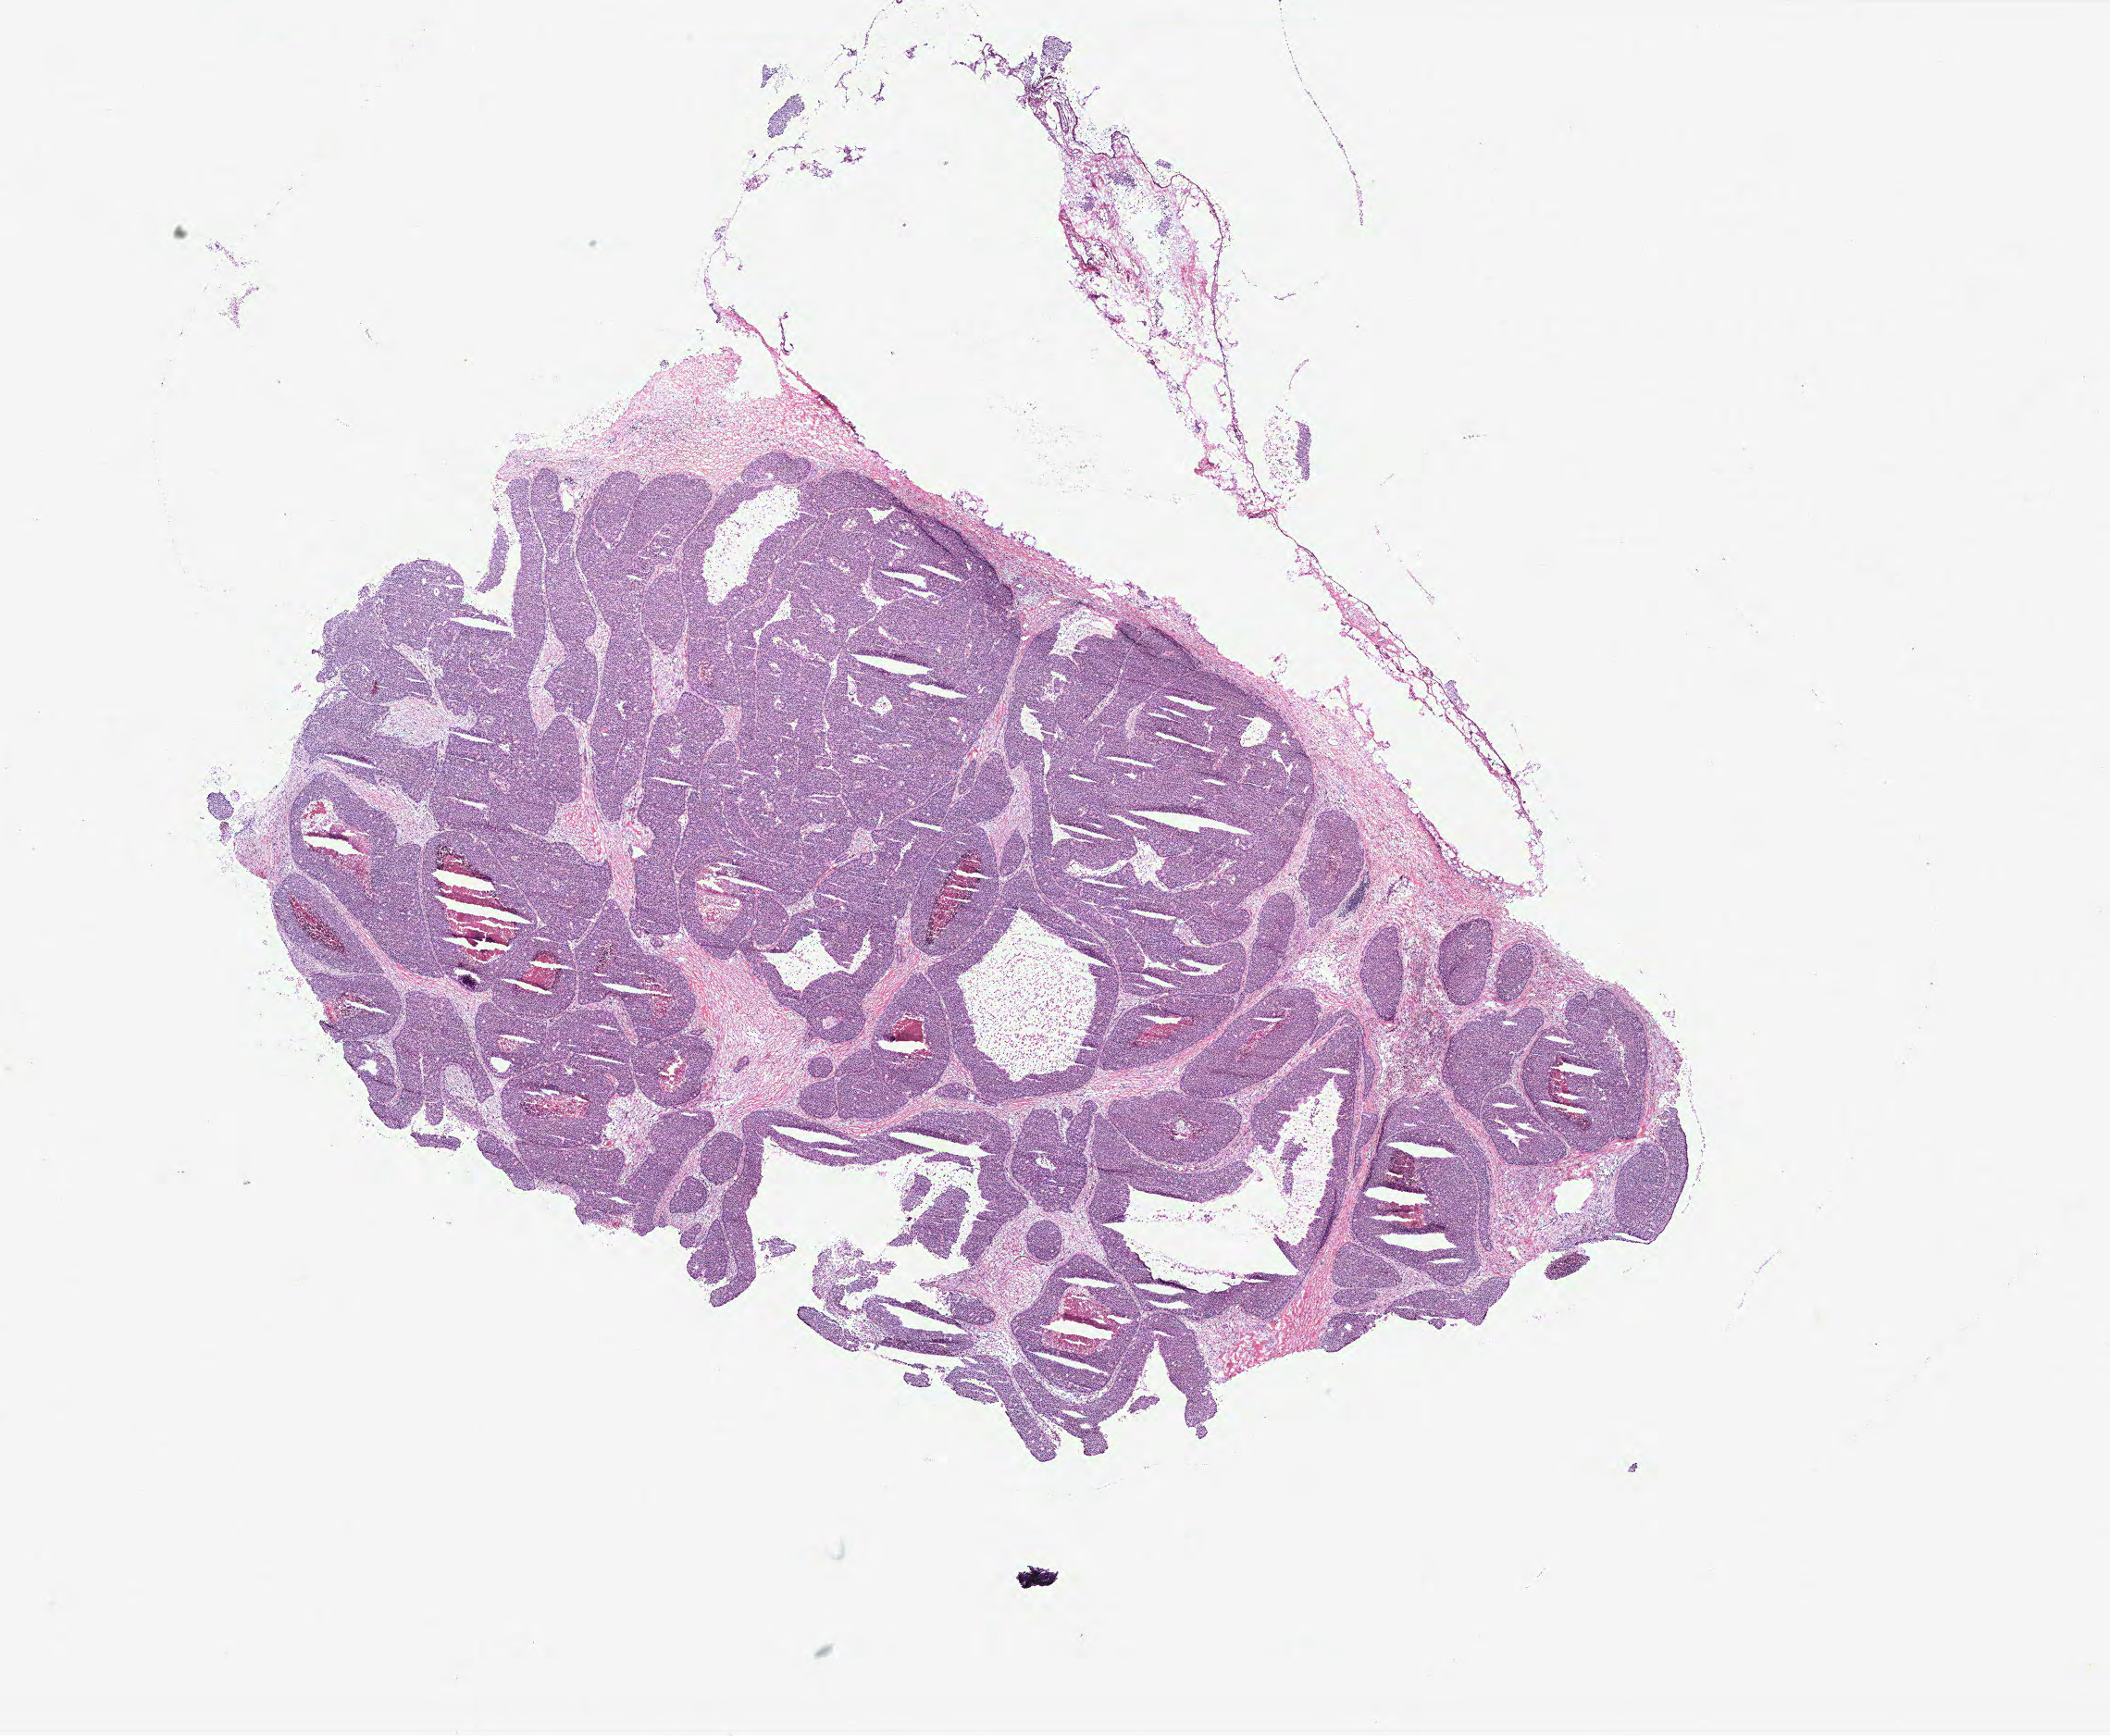
Whole-slide histology image, H&E-stained — shown as a low-resolution overview of the whole scanned area (about 18.2 x 15.0 mm). Breast, tumour tissue. Female, 46 y/o.
Histologic diagnosis: Infiltrating duct carcinoma, NOS.